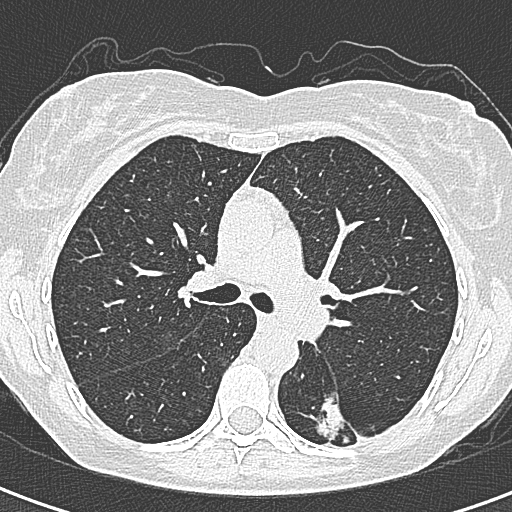
Chest CT (low-dose screening protocol), one axial image. First (baseline) screen. Lung window (W 1500 / L -600 HU). 1 mm slice thickness. 120 kVp. Female participant, aged 58 years at enrolment. Former smoker at enrolment.
Lesion marked by an expert reader, bounding box (x1, y1, x2, y2) in pixels: (291, 390, 361, 454). The screening reader recorded 2 non-calcified nodules or masses ≥4 mm on this exam (left lower lobe, right lower lobe); which of them this box marks is not recorded. Later outcome: lung cancer diagnosed 22 days after this screen — adenocarcinoma, NOS, left lower lobe, moderately differentiated (G2), stage IA (AJCC 6th edition), 25 mm at pathology.